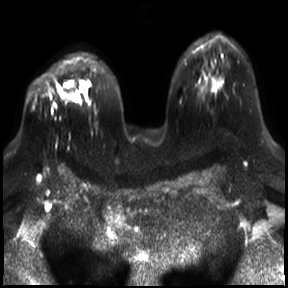
Breast MRI, one axial slice; position 21 of 30 along the scan axis; diffusion-weighted series; image 2 of 4 stored at this slice position (different b-values; order by instance number); 3 T; 4 mm slice thickness; 288 × 288 image matrix, field of view 340 × 340 mm. Female patient.
Structures marked on this image (outlined manually by an expert reader):
- tumour on diffusion-weighted imaging: bounding box <60,81,73,99> (left, top, right, bottom; pixels)